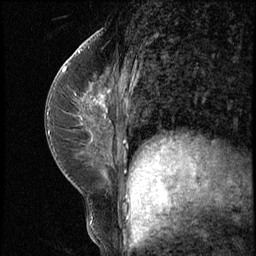
Breast MRI (dynamic contrast-enhanced), one sagittal slice. Slice 28 of 62 in the series (ordered by position). 3 images stored at this slice position (order not interpretable as contrast timing). 1.5 T. TE 4.2 ms, TR 8.7 ms. 2.5 mm slice thickness. 256 × 256 image matrix, field of view 180 × 180 mm. Patient: female, 35 years. Case-level facts recorded for this patient, not image findings: setting: breast cancer imaged before/during neoadjuvant chemotherapy; receptor status: HER2-positive.
Outlined on this slice (semi-automatic segmentation, software-assisted and operator-edited):
- analysis volume of interest (the breast-tissue region the enhancement analysis was run in; not a lesion): bounding box <71,78,120,139> (left, top, right, bottom; pixels)
- tumour enhancement mask (voxels above the 140 % enhancement threshold inside the analysis volume of interest): <100,95,104,104>